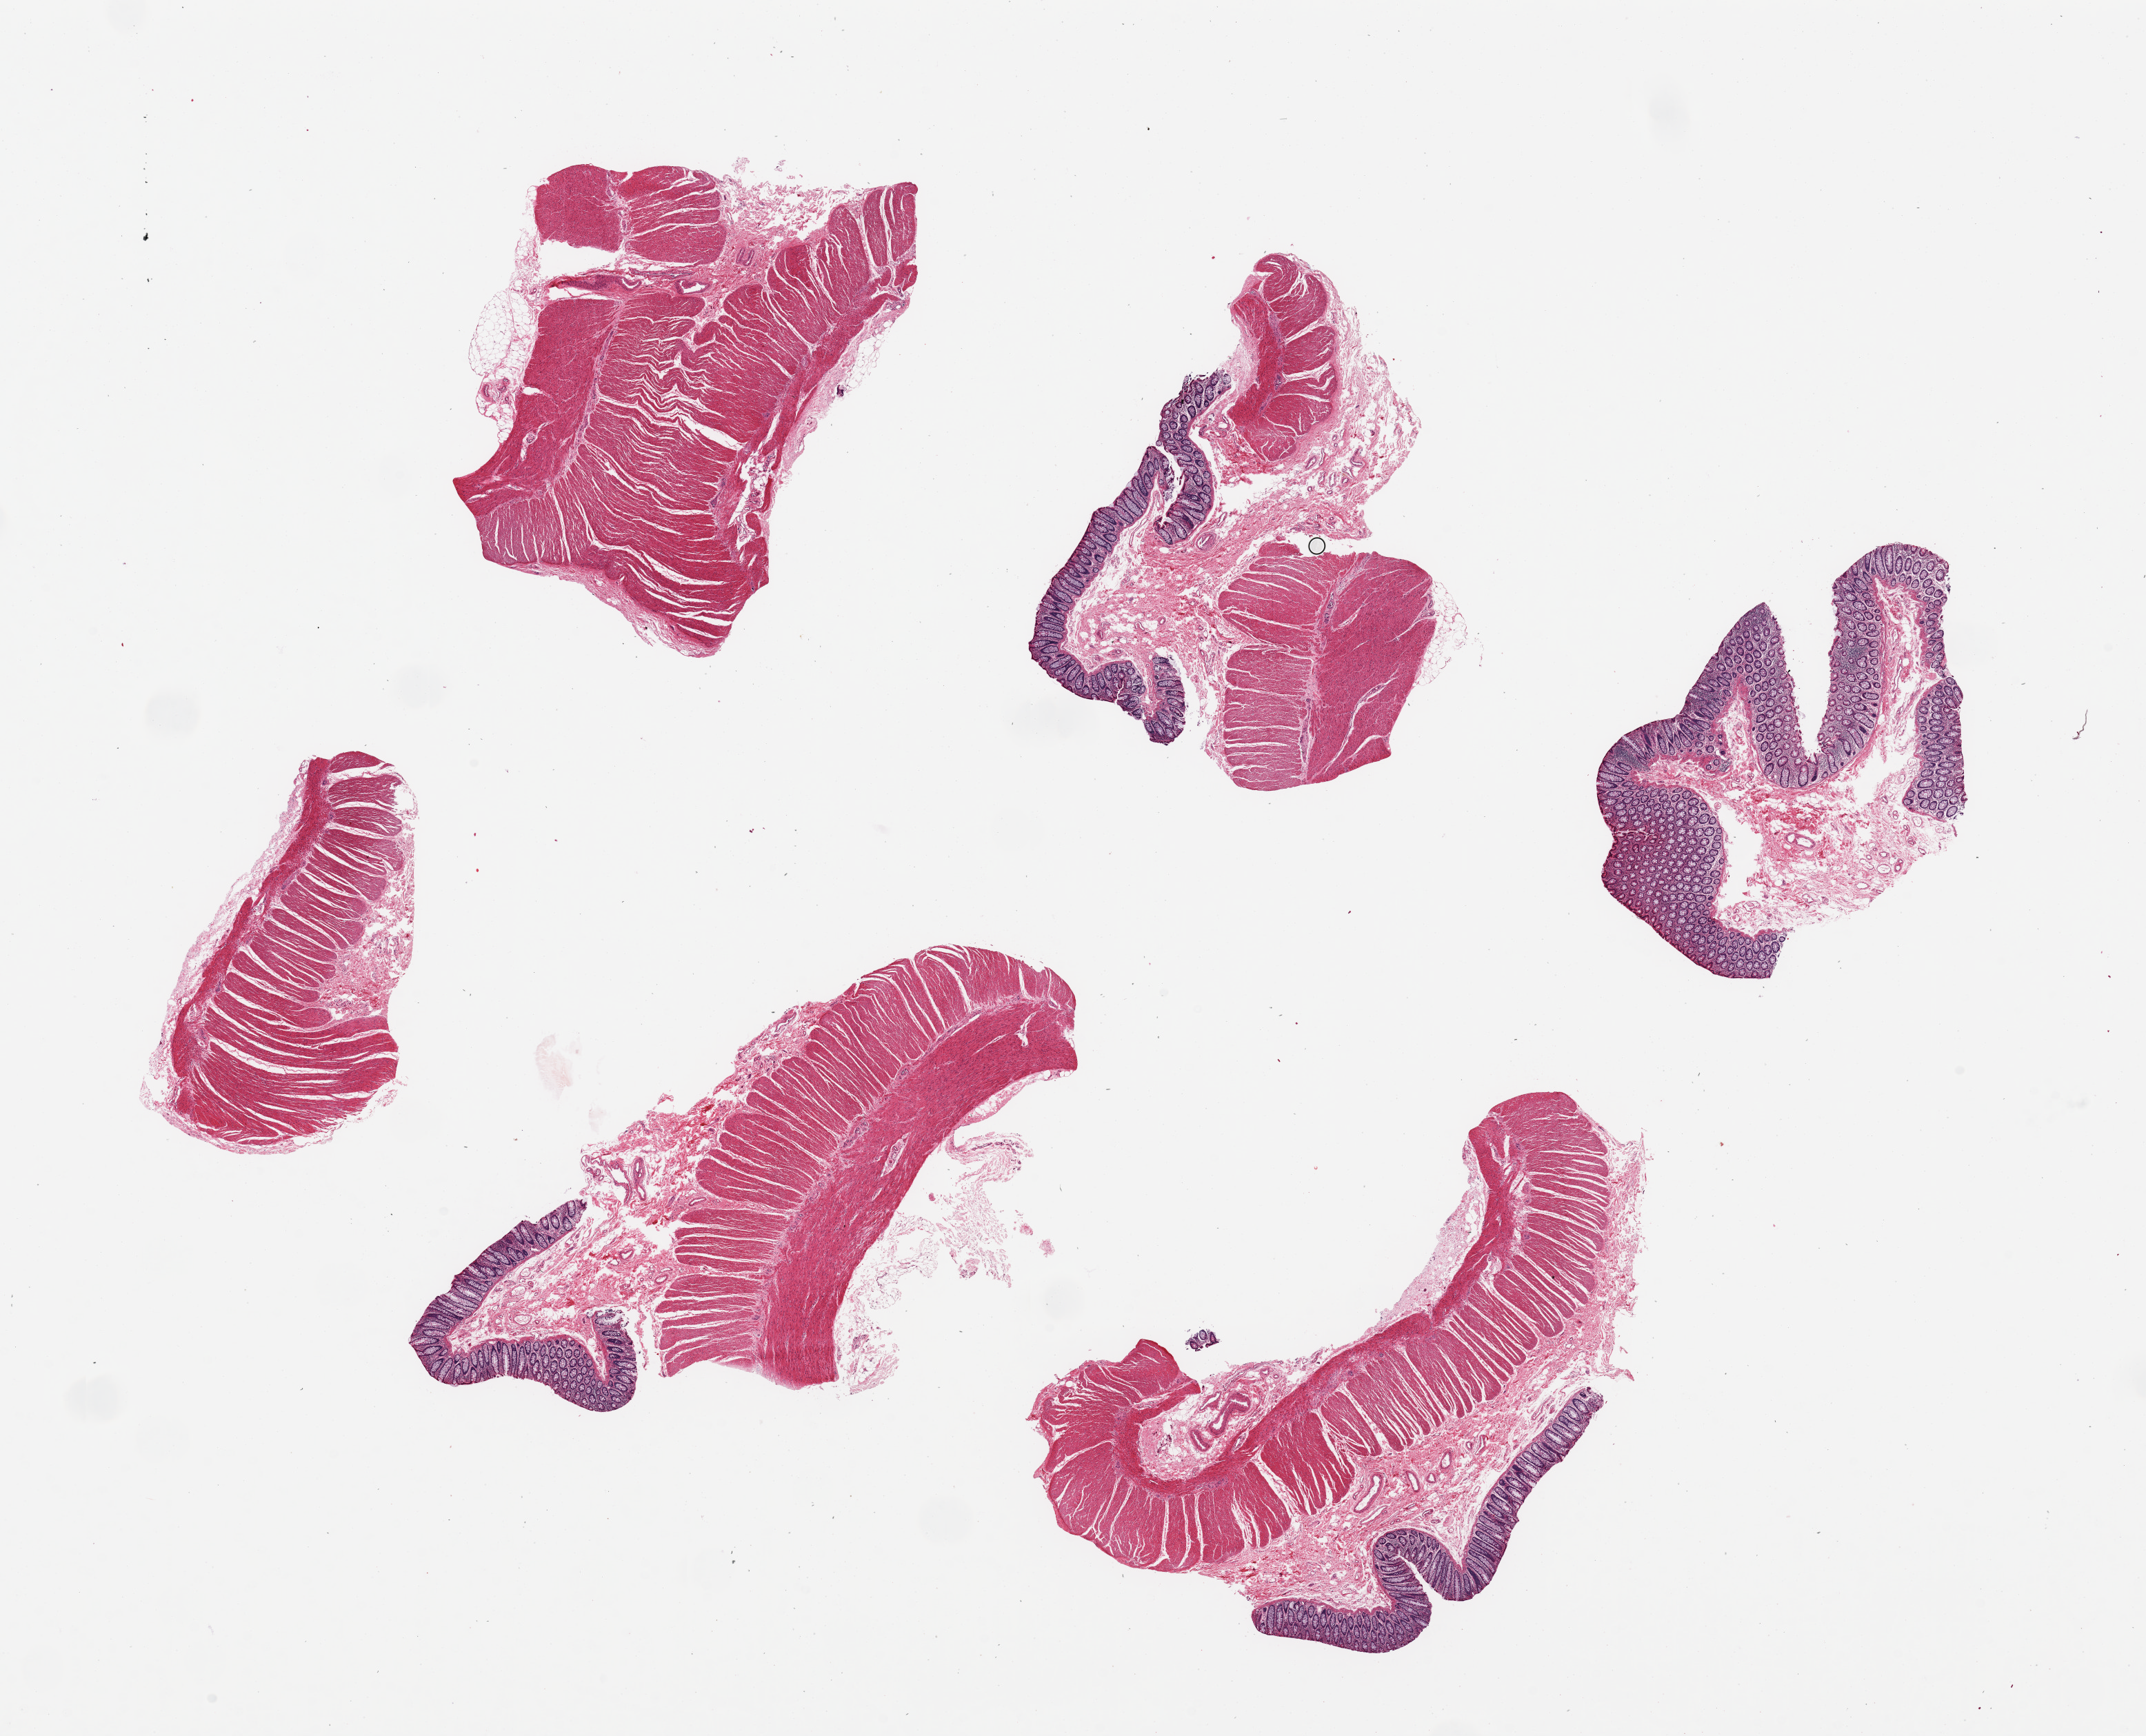
H&E whole-slide image, brightfield, a low-resolution overview of the entire scanned area, about 24.6 x 19.9 mm; PAXgene-fixed, paraffin-embedded tissue; target tissue: transverse colon; donor tissue sample. Donor: male.
Review note (as recorded): 6 pieces, ~6x3mm mucosa remarkably well-preserved, up to 500 microns thick.